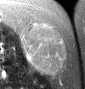
MRI of an extremity soft-tissue mass, one axial slice; slice 20 of 46 in the series (ordered by position); T2-weighted fat-saturated; MR volume resampled by the dataset authors to the PET/CT grid (not the native acquisition matrix); 3.27 mm slice thickness; 85 × 89 image matrix, field of view 83 × 87 mm. Female patient. From the clinical record (not read from this slice): histological type: leiomyosarcoma; grade: intermediate; site of the primary tumour: parascapusular.
Structures marked on this image (expert contour drawn on MRI and transferred to this co-registered scan by the dataset authors):
- gross tumour volume including surrounding oedema: bounding box <20,23,67,74> (left, top, right, bottom; pixels)
- gross tumour volume (mass): <20,23,67,74>